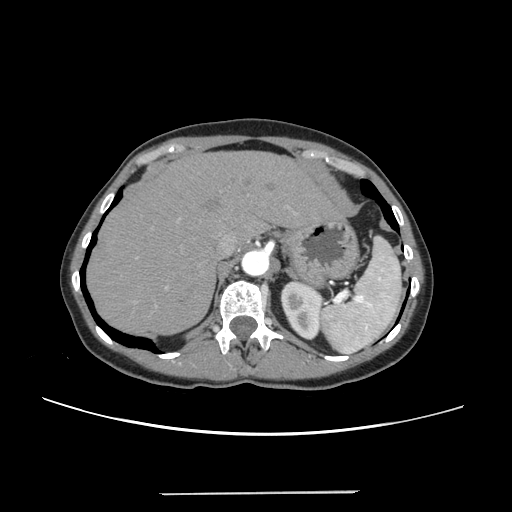
Contrast-enhanced abdominal CT, one axial slice; position 187 of 240 along the scan axis; 120 kVp; intravenous contrast given; soft-tissue window (W 400 / L 40 HU); 1.25 mm slice thickness; 512 × 512 image matrix, field of view 371 × 371 mm. Female patient, age 60 years. From the clinical record (not read from this slice): diagnosis: colorectal cancer liver metastases, imaged before liver resection; multiple liver metastases: no; largest metastasis: 1.5 cm; disease in both lobes: no.
Annotated regions visible in this slice (manually delineated by an expert):
- hepatic veins: bounding box <220,234,236,254> (left, top, right, bottom; pixels)
- liver: <88,152,336,335>
- planned liver remnant (the part of the liver to remain after resection): <88,152,336,336>
- portal vein (with intrahepatic branches): <165,206,289,288>